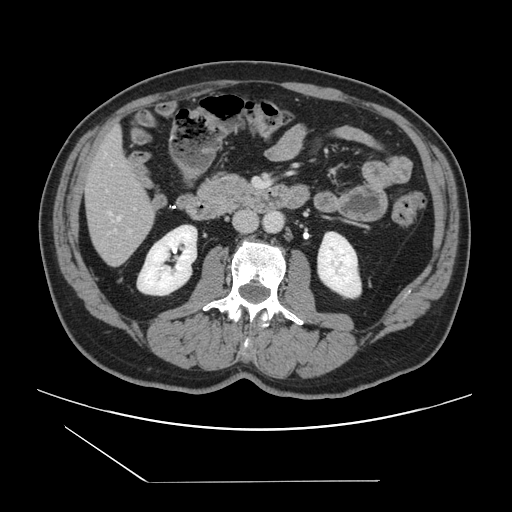
Contrast-enhanced abdominal CT, one axial slice. Position 41 of 157 along the scan axis. 120 kVp. Intravenous contrast given. Soft-tissue window (W 400 / L 40 HU). 512 × 512 image matrix, field of view 407 × 407 mm. Male patient, age 61 years. Case-level facts recorded for this patient, not image findings: diagnosis: colorectal cancer liver metastases, imaged before liver resection; multiple liver metastases: yes; largest metastasis: 5.5 cm; chemotherapy before resection: no.
Annotated regions visible in this slice (outlined manually by an expert reader):
- hepatic veins: bounding box [x1, y1, x2, y2] px = [110, 212, 121, 231]
- liver: [85, 130, 155, 265]
- planned liver remnant (the part of the liver to remain after resection): [85, 131, 152, 218]
- portal vein (with intrahepatic branches): [129, 230, 131, 232]